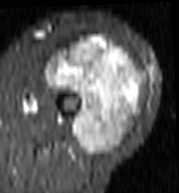
MRI of an extremity soft-tissue mass, one axial slice. STIR. MR volume resampled by the dataset authors to the PET/CT grid (not the native acquisition matrix). 3.27 mm slice thickness. 179 × 193 image matrix, field of view 175 × 188 mm. Female patient. From the clinical record (not read from this slice): histological type: undifferentiated – high grade; grade: high; site of the primary tumour: left thigh.
Structures marked on this image (expert contour drawn on MRI and transferred to this co-registered scan by the dataset authors):
- gross tumour volume including surrounding oedema: box from (x=47, y=37) to (x=142, y=156) px
- gross tumour volume (mass): (x=47, y=37)–(x=142, y=156)